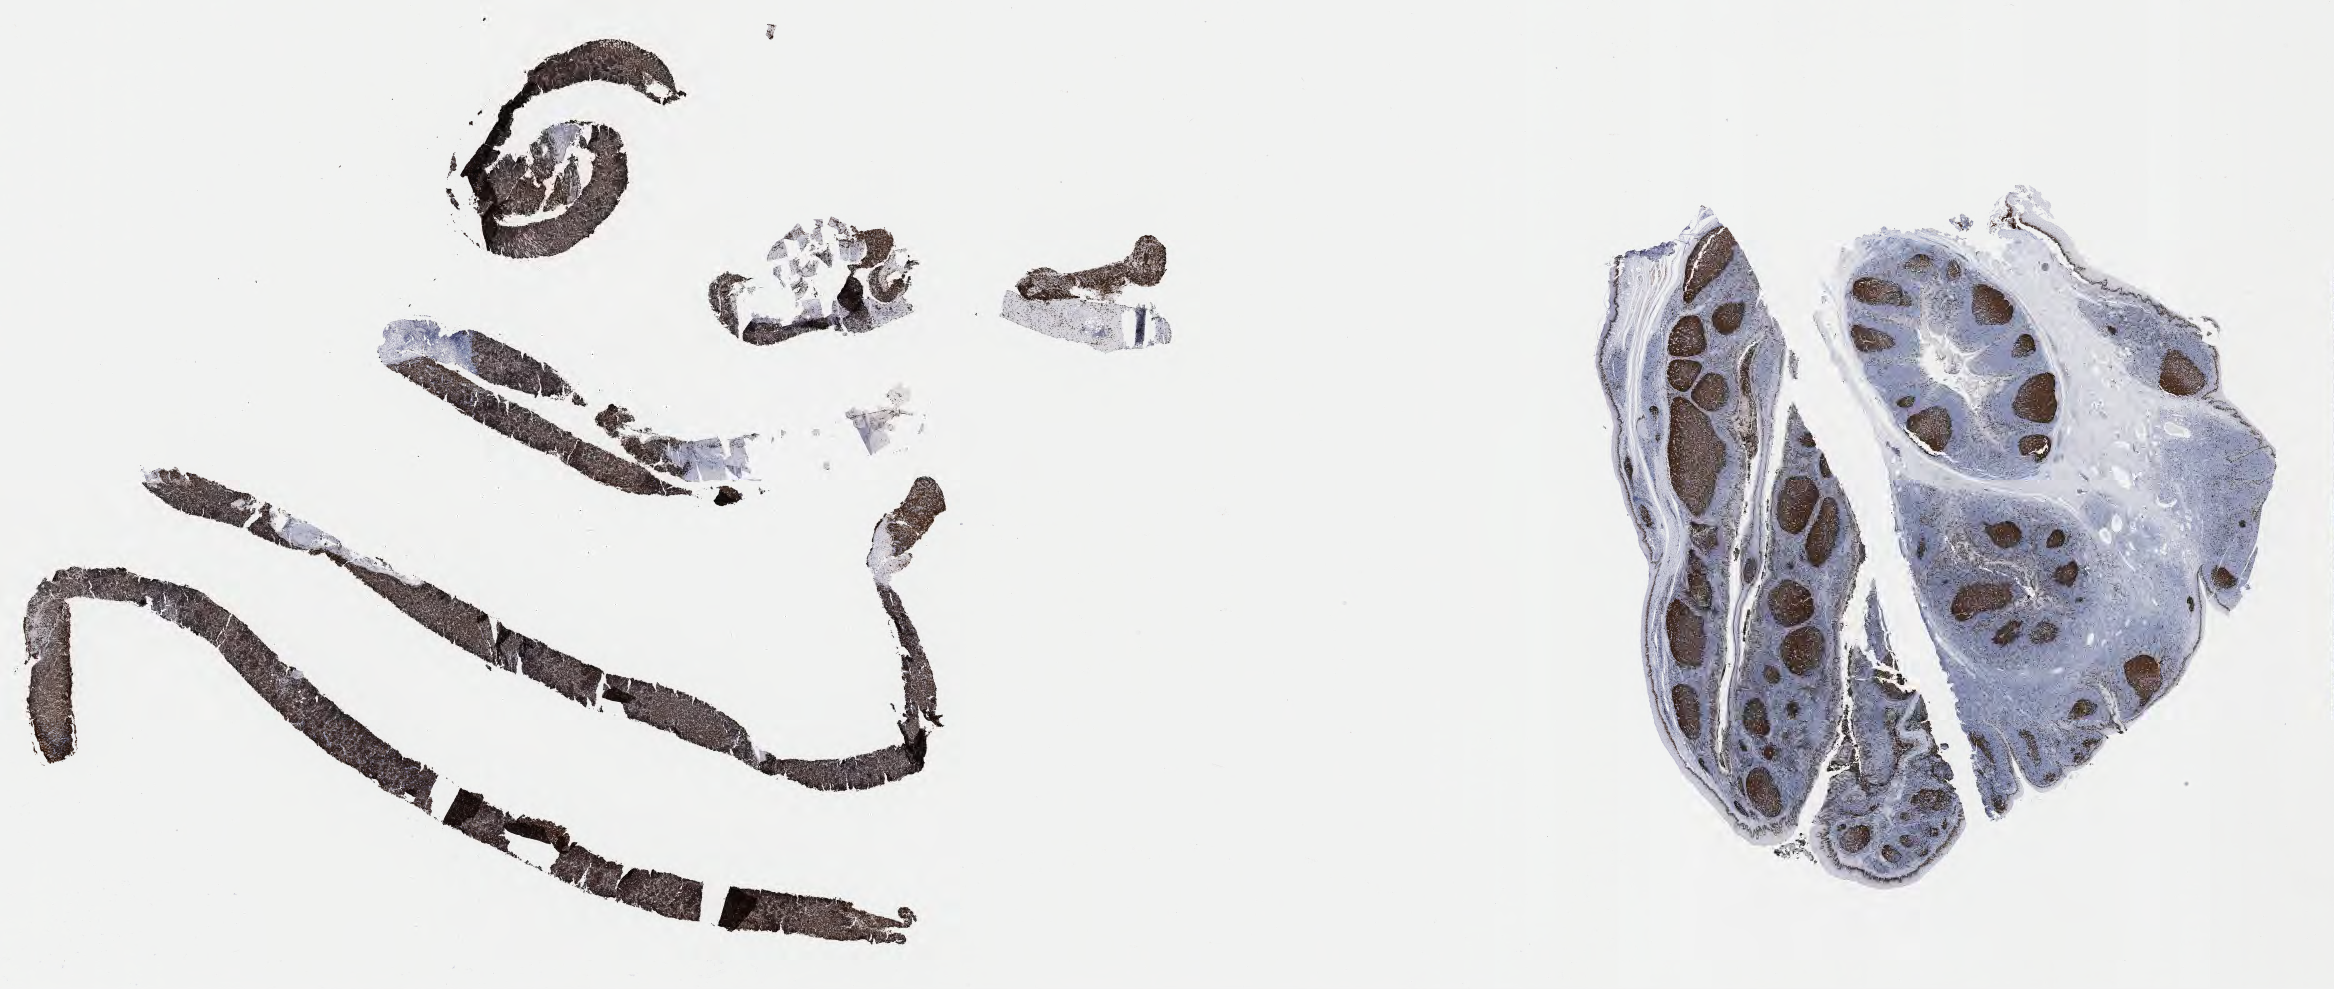
Immunohistochemistry (IHC) whole-slide image stained for Ki-67 — low-resolution overview of the scanned area, about 37.8 x 16.0 mm; specimen: tumor tissue. Male patient, age 45 years.
Diagnosis: Burkitt lymphoma, NOS.